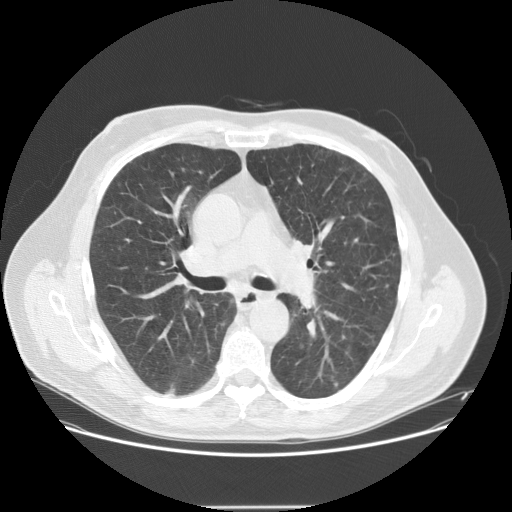
Low-dose screening chest CT, one axial slice; position 88 of 143 along the scan axis; reconstruction kernel STANDARD; 120 kVp; lung window (W 1500 / L -600 HU); 2.5 mm slice thickness; 512 × 512 image matrix.
Structures marked on this image (manually delineated by an expert):
- lesion 3 (tumor, lower lobe of right lung): bounding box <166,384,176,395> (left, top, right, bottom; pixels)